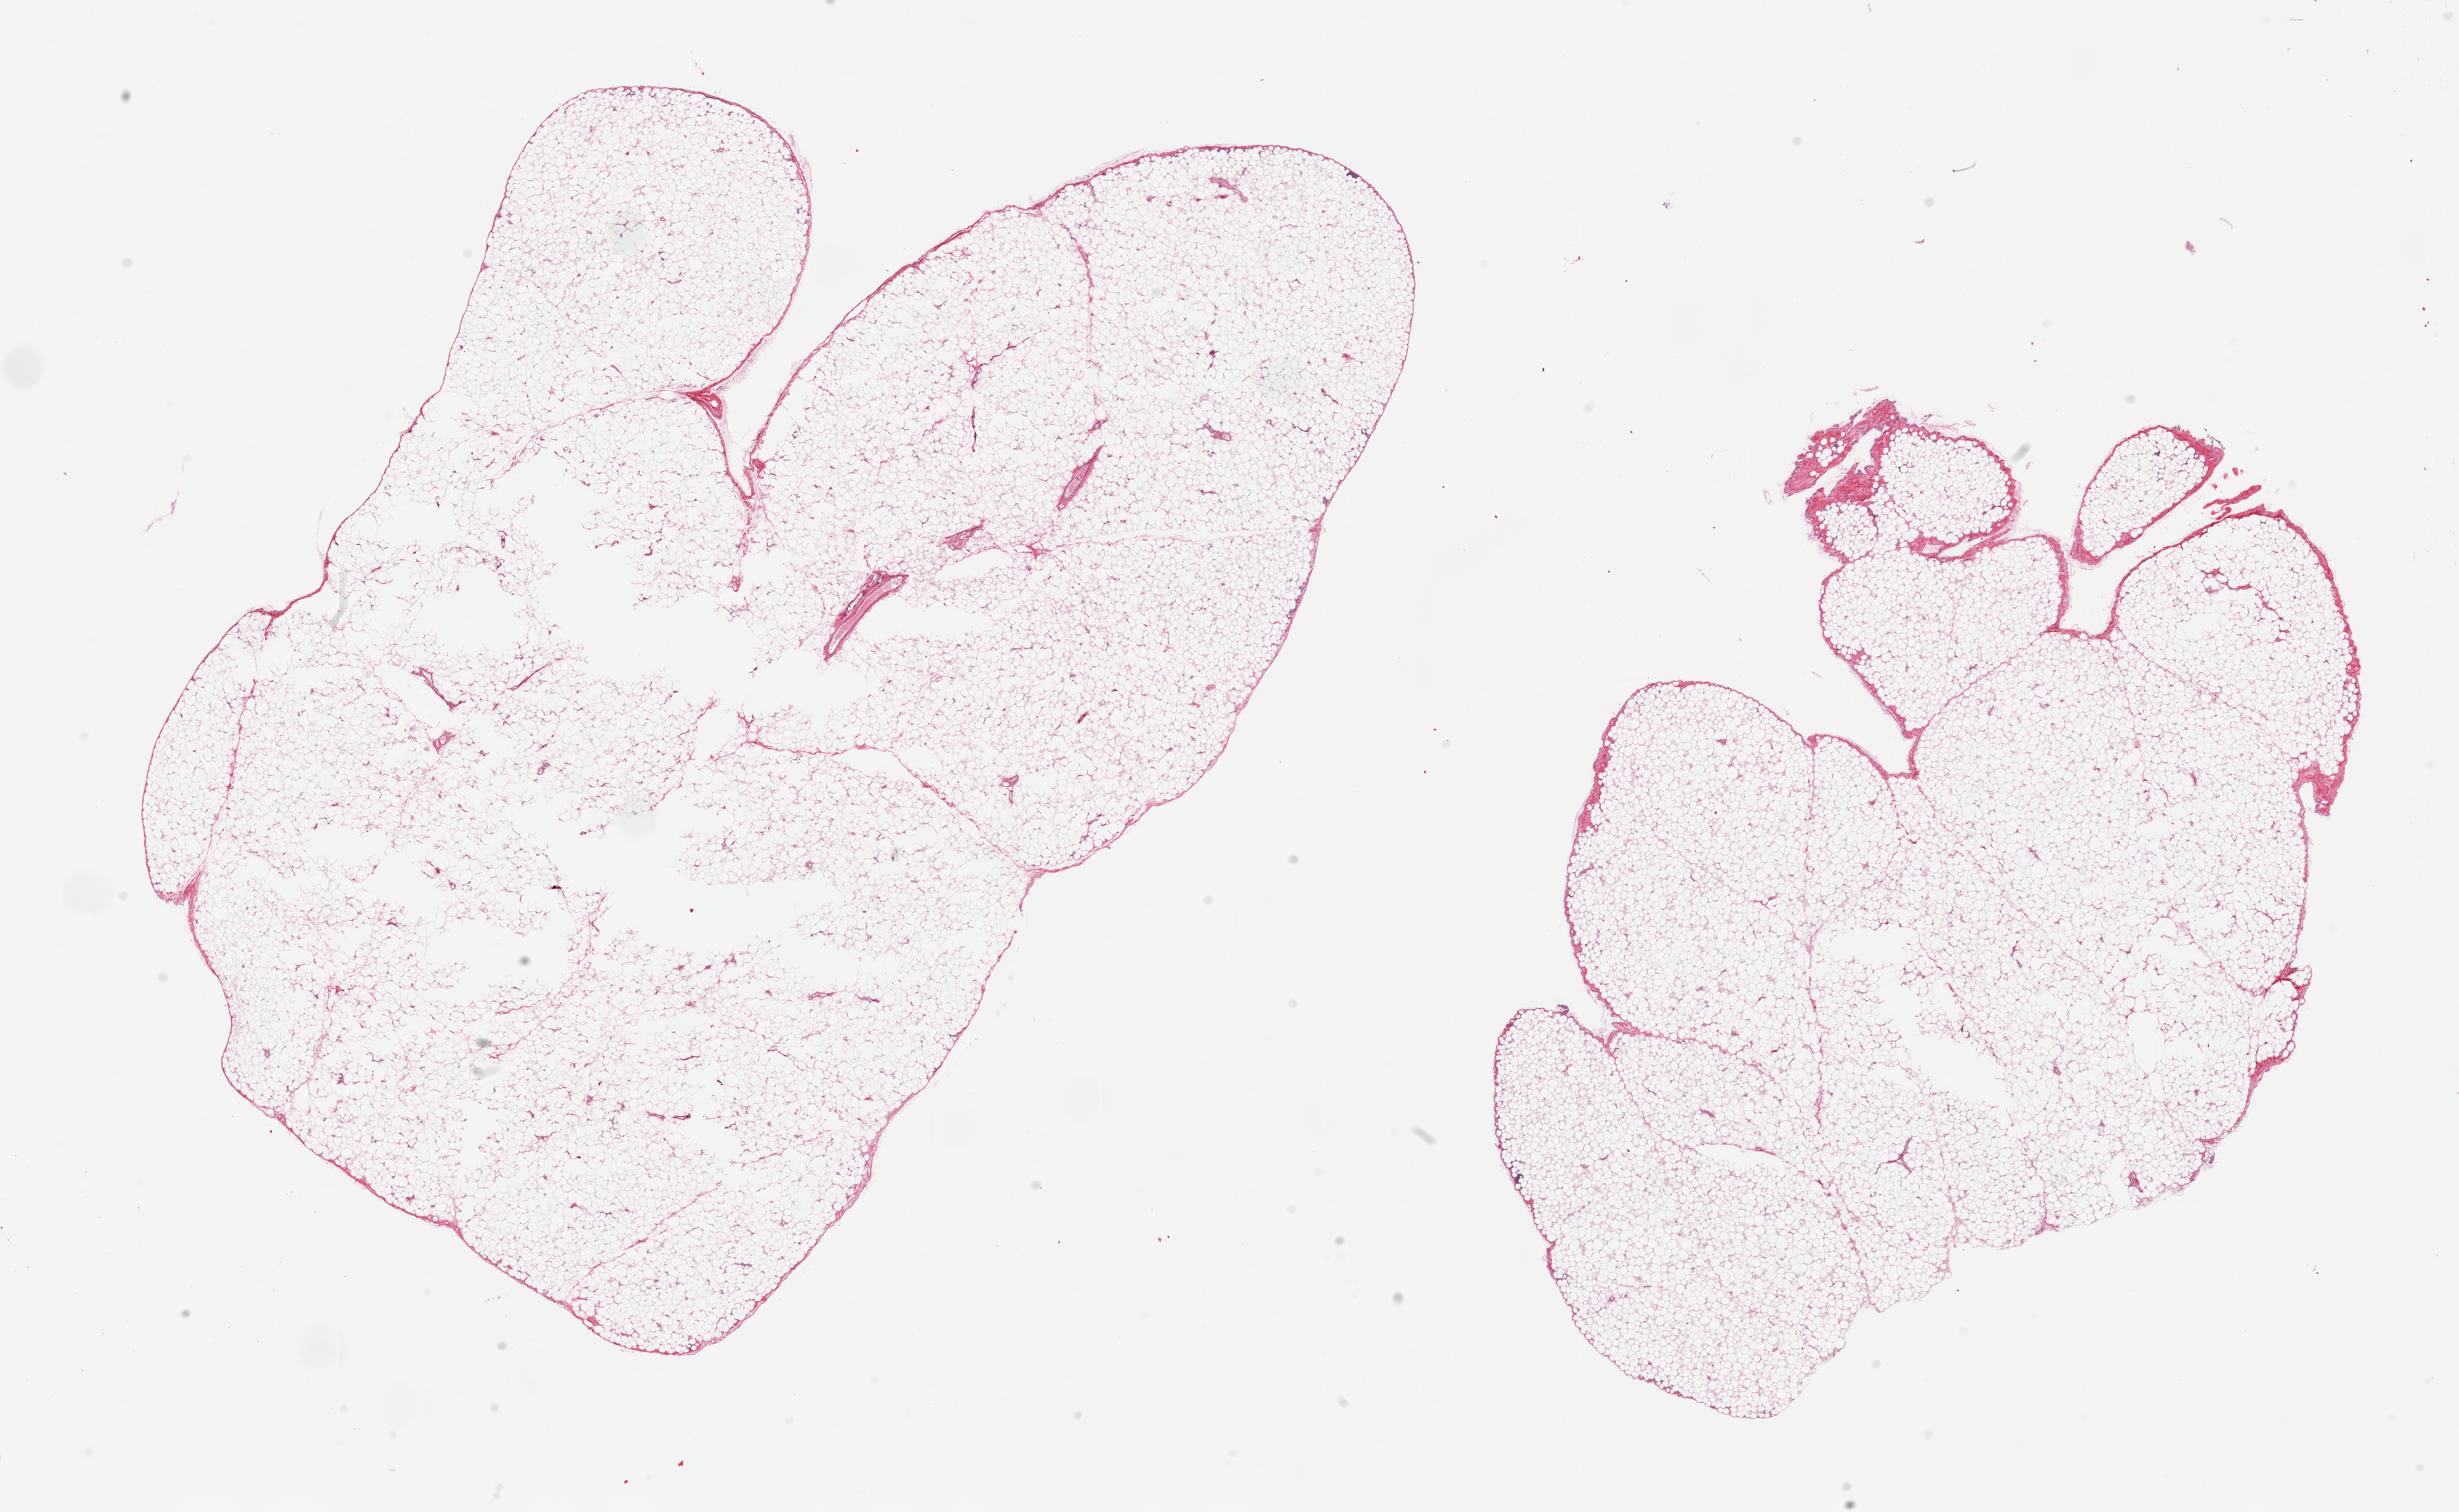
Whole-slide image, H&E stain — shown as a low-resolution overview of the whole scanned area (about 28.5 x 17.6 mm, acquisition: 20x scan); PAXgene-fixed, paraffin-embedded tissue; section of omentum (target tissue); tissue donor sample. Donor: male.
- review note (as recorded): 2 pieces, minimal fibrous tissue